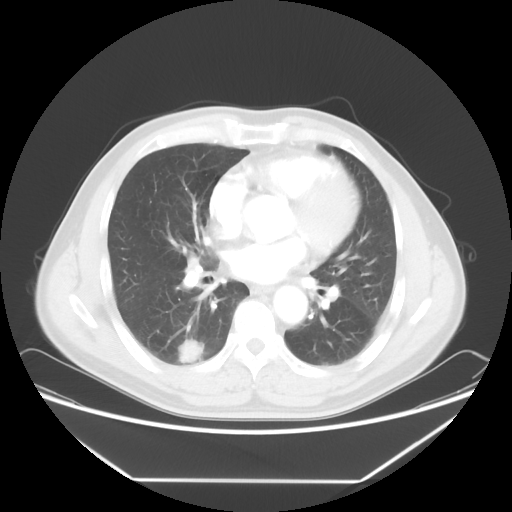
Chest CT, one axial slice; position 32 of 65 along the scan axis; reconstruction kernel STANDARD; lung window (W 1500 / L -600 HU); 5 mm slice thickness; 512 × 512 image matrix, field of view 418 × 418 mm. Male patient, age 50 years. Case-level facts recorded for this patient, not image findings: clinical TNM (as recorded): T1c N0 M0; histopathological grade: G3.
Structures marked on this image (bounding box drawn by a radiologist):
- lung tumour (recorded histology: adenocarcinoma): box from (x=172, y=336) to (x=209, y=364) px